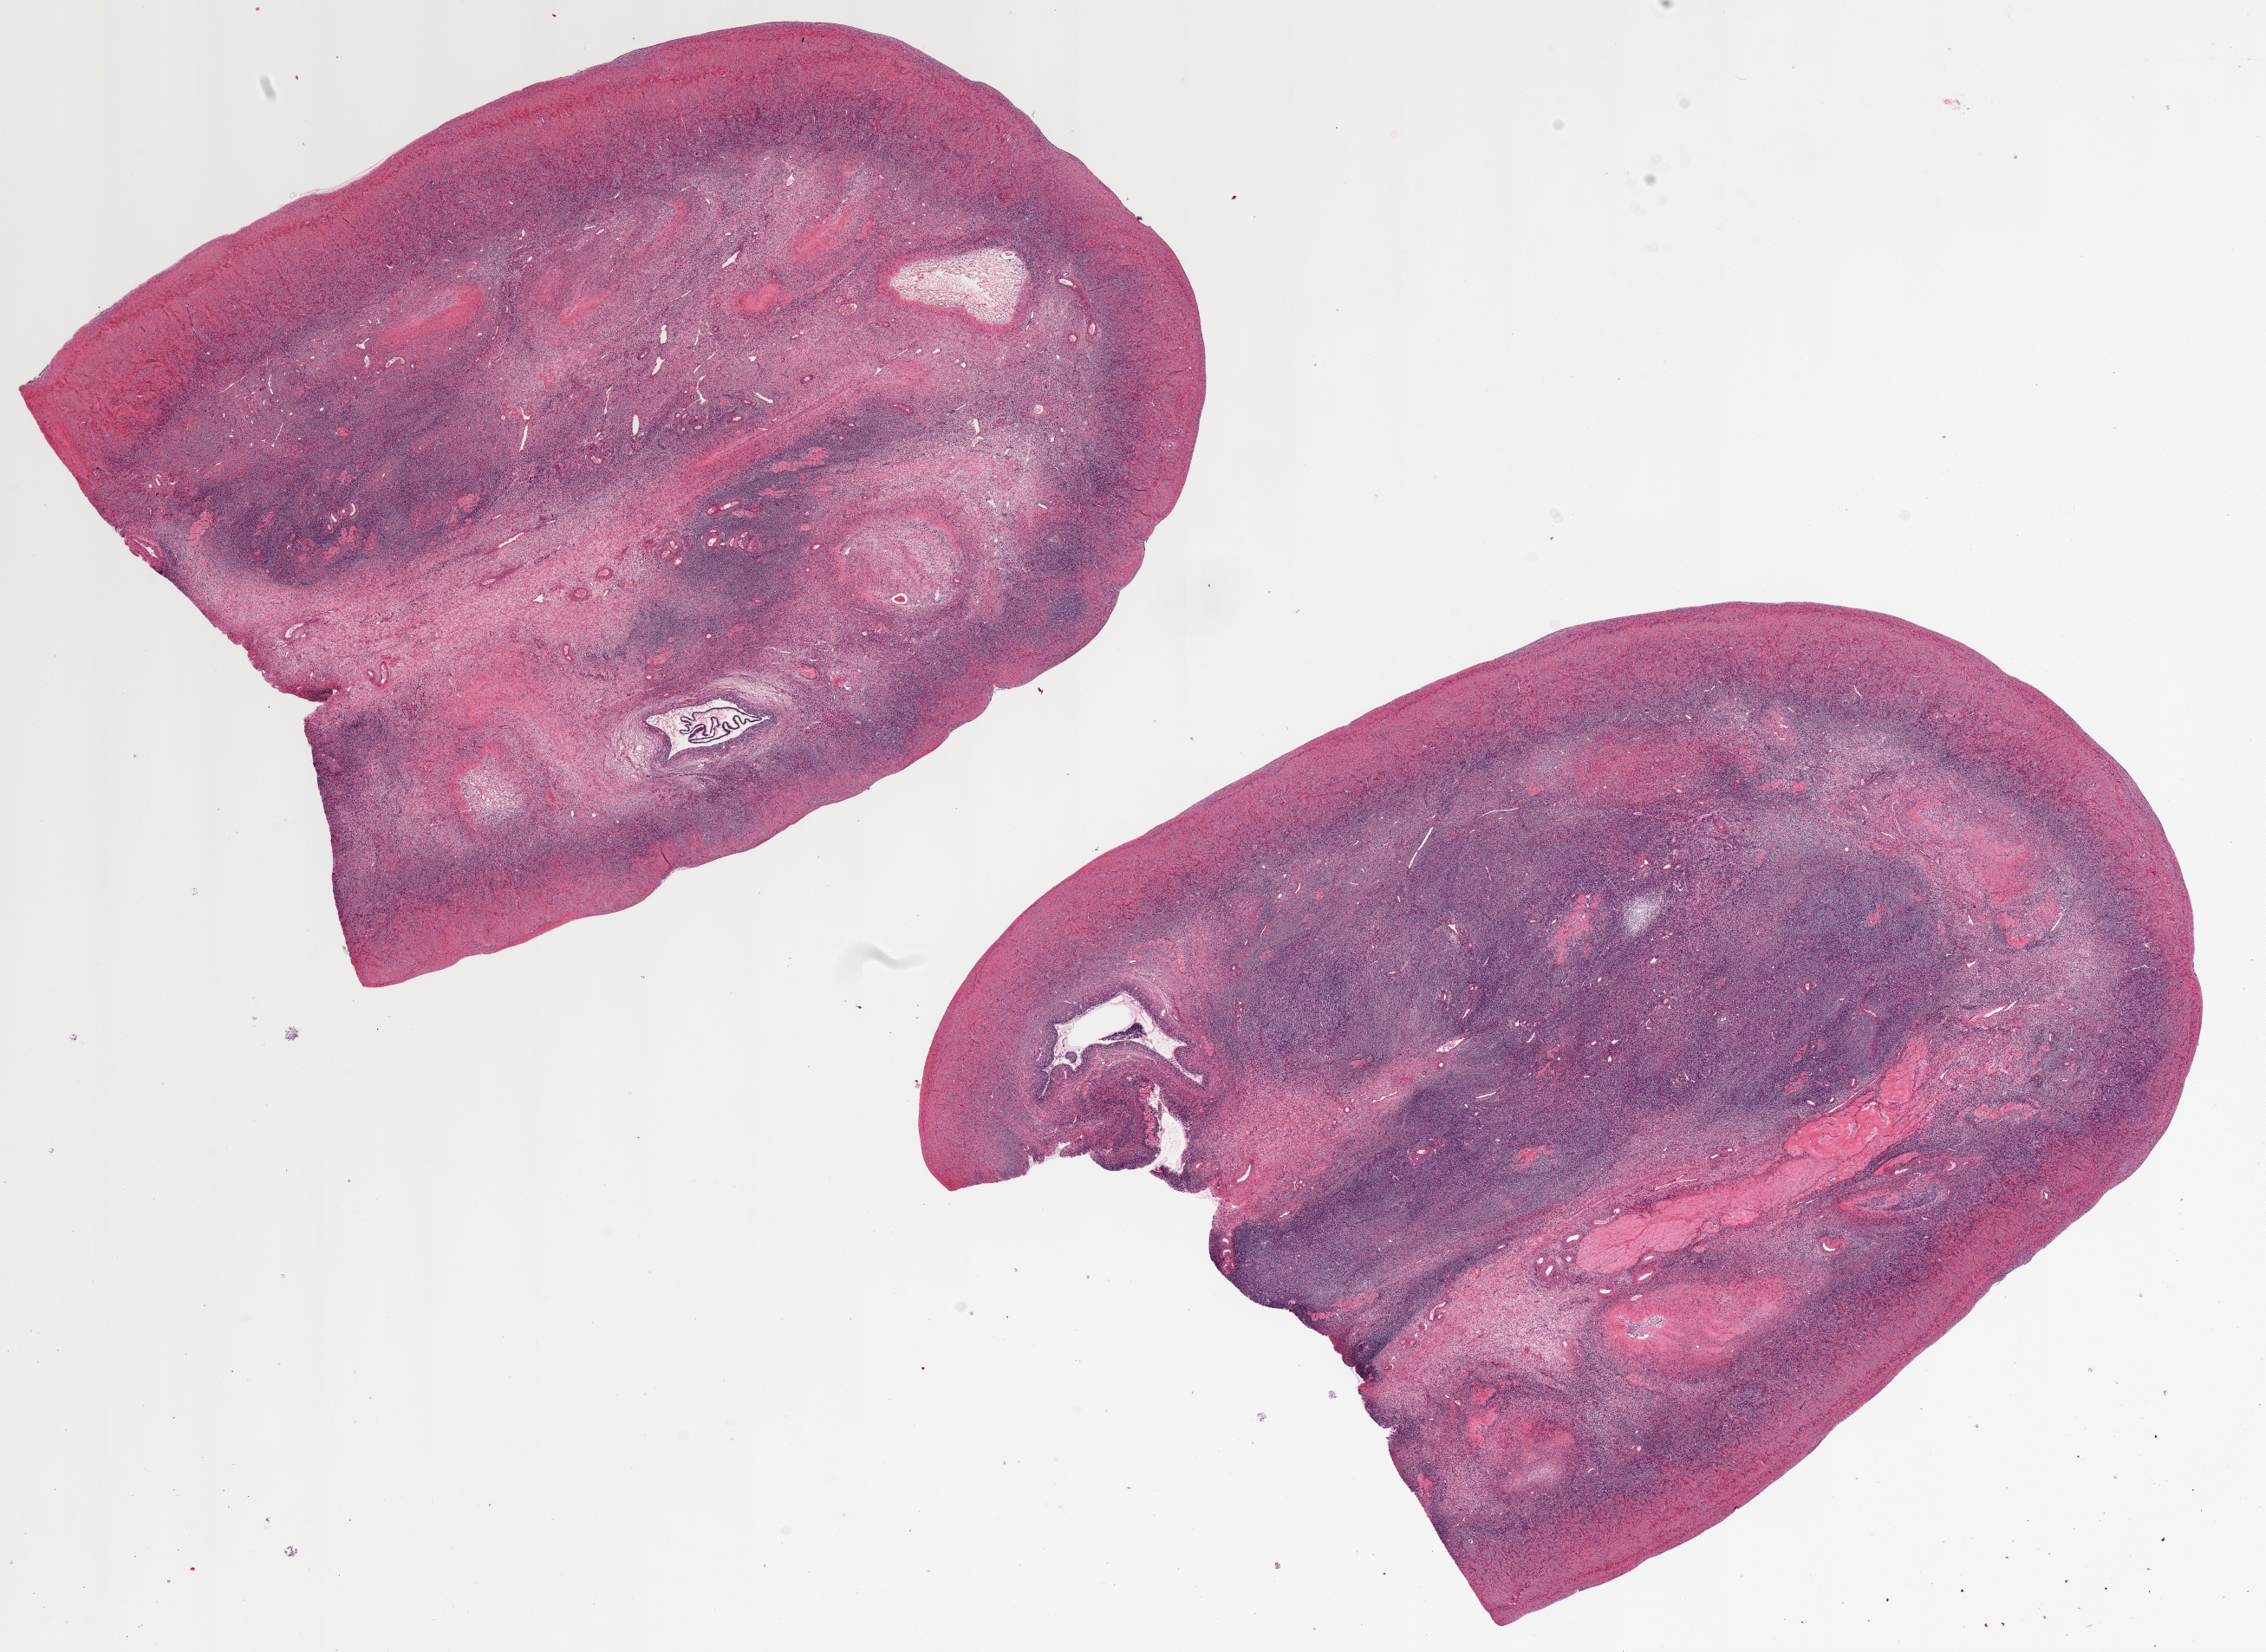
Digitized haematoxylin and eosin-stained section — low-resolution overview of the scanned area, about 20.7 x 15.1 mm, PAXgene-fixed, paraffin-embedded tissue, section of ovary (target tissue), donor tissue sample. Donor sex: female.
- reviewer comment on this tissue sample: 2 9x8mm aliquots. Post-menopausal-appearing, remote corpora albicantia present